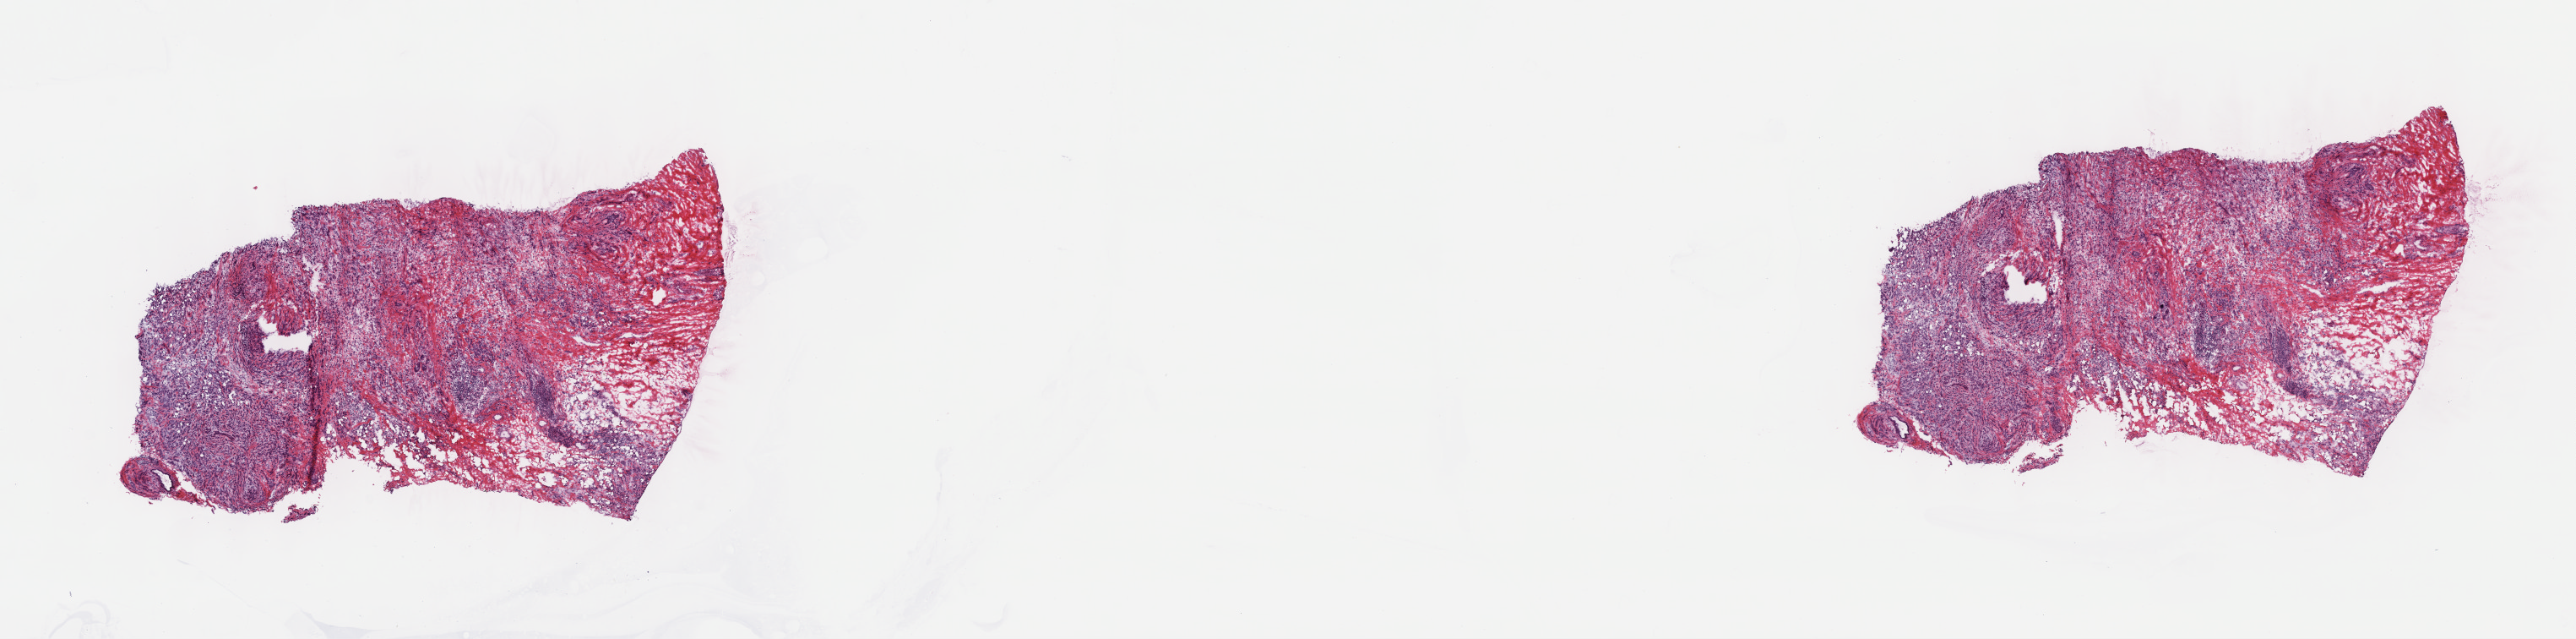
Digitized H&E-stained tissue section (whole slide), whole scanned area (about 24.7 x 6.1 mm, from a 40x scan) shown as a low-resolution overview; frozen section from the top of the tissue portion; sample: primary tumour, breast. Female, age 46 years at initial diagnosis. Composition of this section per pathologist review: tumour cells 100%, tumour nuclei 65%.
Histologic diagnosis: Lobular carcinoma, NOS.